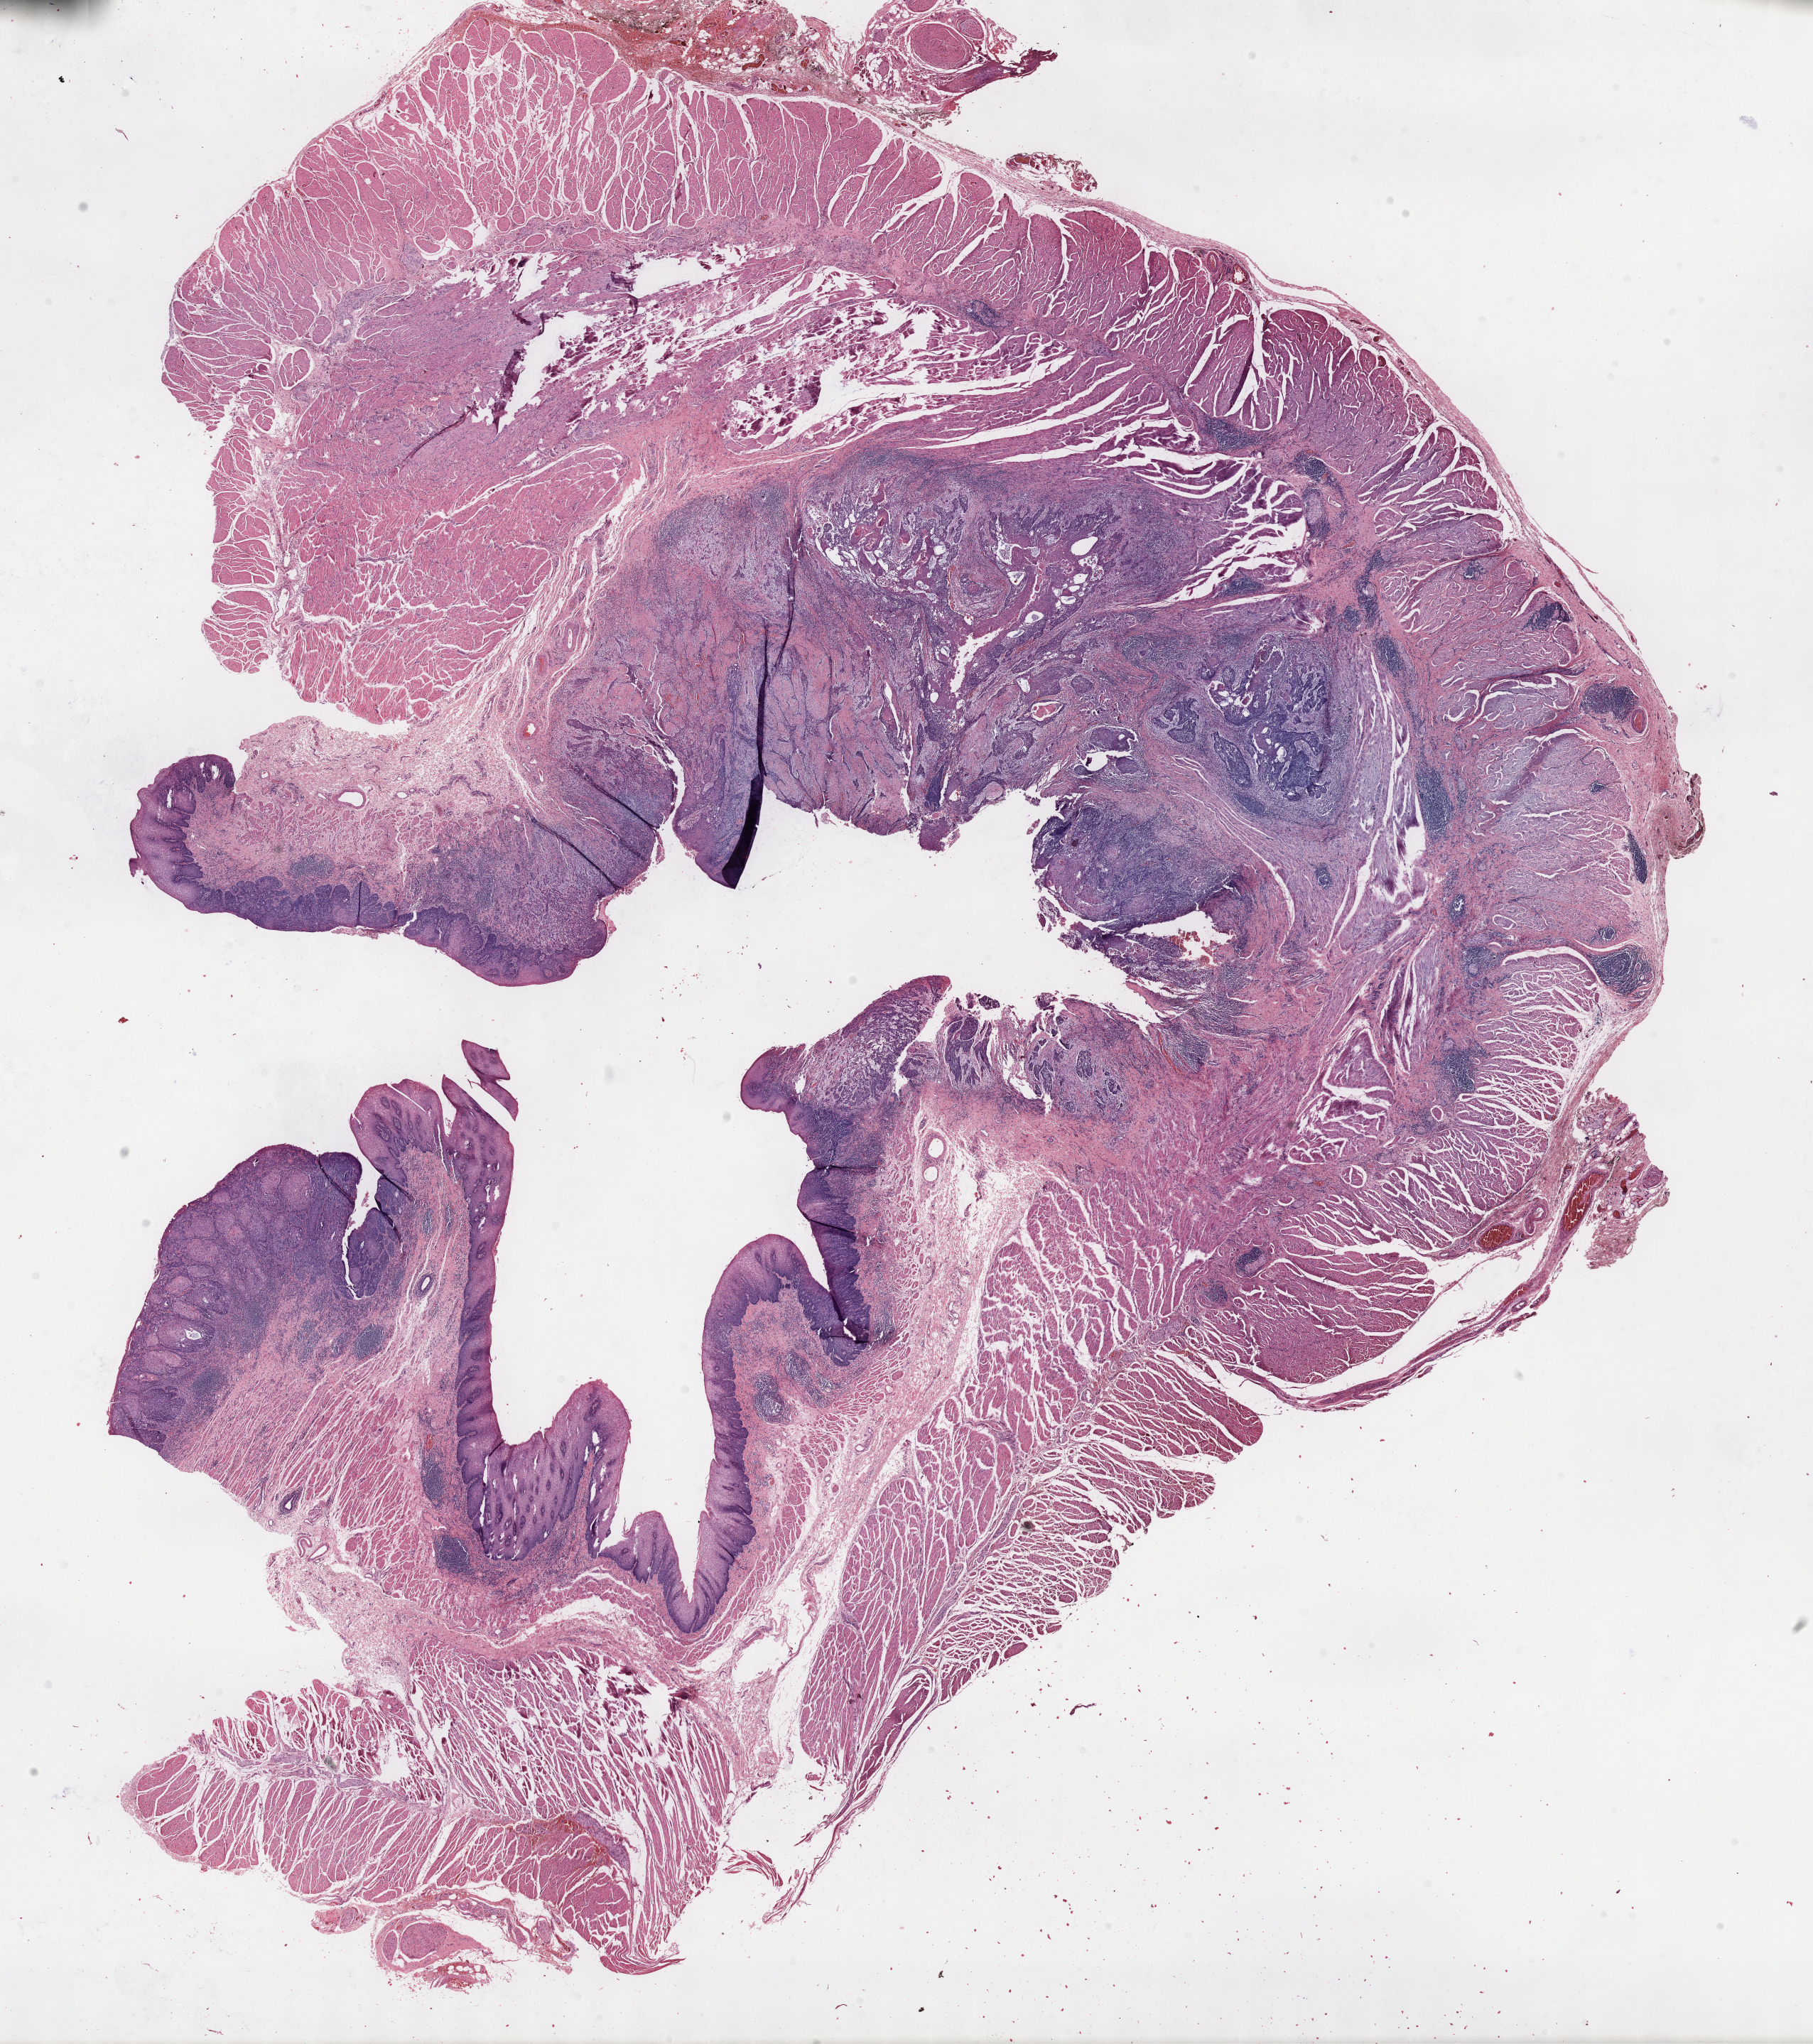
Whole-slide histology image, H&E-stained — whole scanned area (about 20.6 x 23.3 mm, slide scanned at 40x) shown as a low-resolution overview; formalin-fixed paraffin-embedded (FFPE) diagnostic section; primary tumour sample from the esophagus. Female patient; age at initial diagnosis 51 years. Histologic grade: G2 (moderately differentiated).
• AJCC pathologic stage: IIIA
• diagnosis: Squamous cell carcinoma, NOS (middle third of esophagus)
• lymph nodes positive (case pathology): 1 of 25 examined